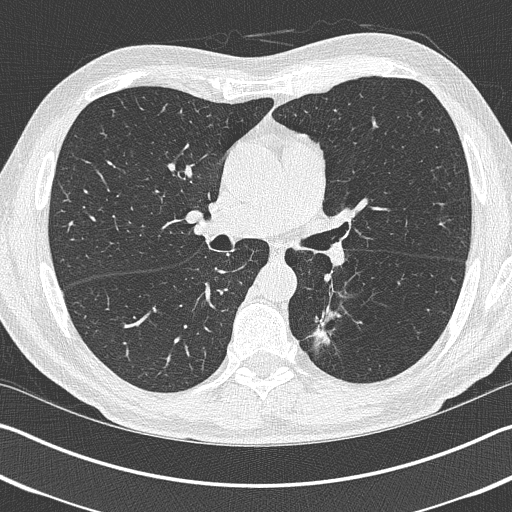
Low-dose screening chest CT, one axial slice. Position 239 of 402 along the scan axis. Lung window (W 1500 / L -600 HU). 1 mm slice thickness. 512 × 512 image matrix.
Annotated regions visible in this slice (outlined manually by an expert reader):
- lesion 1 (tumor, lower lobe of left lung): bounding box <310,312,337,346> (left, top, right, bottom; pixels)